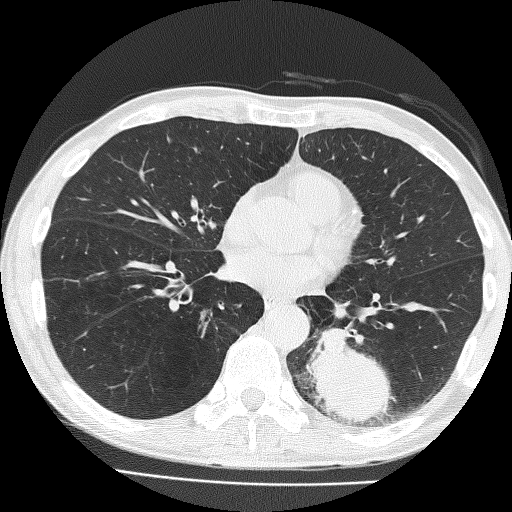
Axial slice from a low-dose chest CT screening exam; baseline screening round; lung window (W 1500 / L -600 HU); slice 87 of 160 in the series; 512 × 512 image matrix, field of view 324 × 324 mm. Male, age 58 years at enrolment.
Expert-annotated lung lesion, bounding box [x1, y1, x2, y2] px = [301, 312, 419, 434]. The screening reader recorded 2 non-calcified nodules or masses ≥4 mm on this exam; which of them this box marks is not recorded. Official screen result: positive, change unspecified: nodule(s) >= 4 mm or enlarging nodule(s), mass(es), or other non-specific abnormalities suspicious for lung cancer.